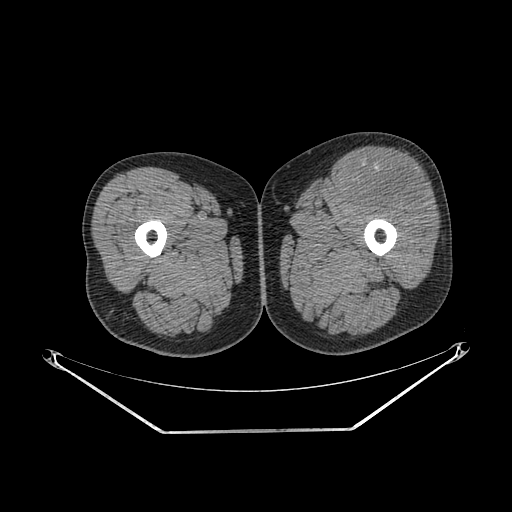
CT of an extremity soft-tissue mass (from a PET/CT study), one axial slice; reconstruction kernel SOFT; soft-tissue window (W 400 / L 40 HU); 3.75 mm slice thickness; 512 × 512 image matrix, field of view 500 × 500 mm. Male patient. From the clinical record (not read from this slice): histological type: extraskeletal osteosarcoma; grade: high; site of the primary tumour: thigh.
Outlined on this slice (expert contour drawn on MRI and transferred to this co-registered scan by the dataset authors):
- gross tumour volume (mass): bounding box (x1, y1, x2, y2) in pixels: (354, 160, 430, 211)